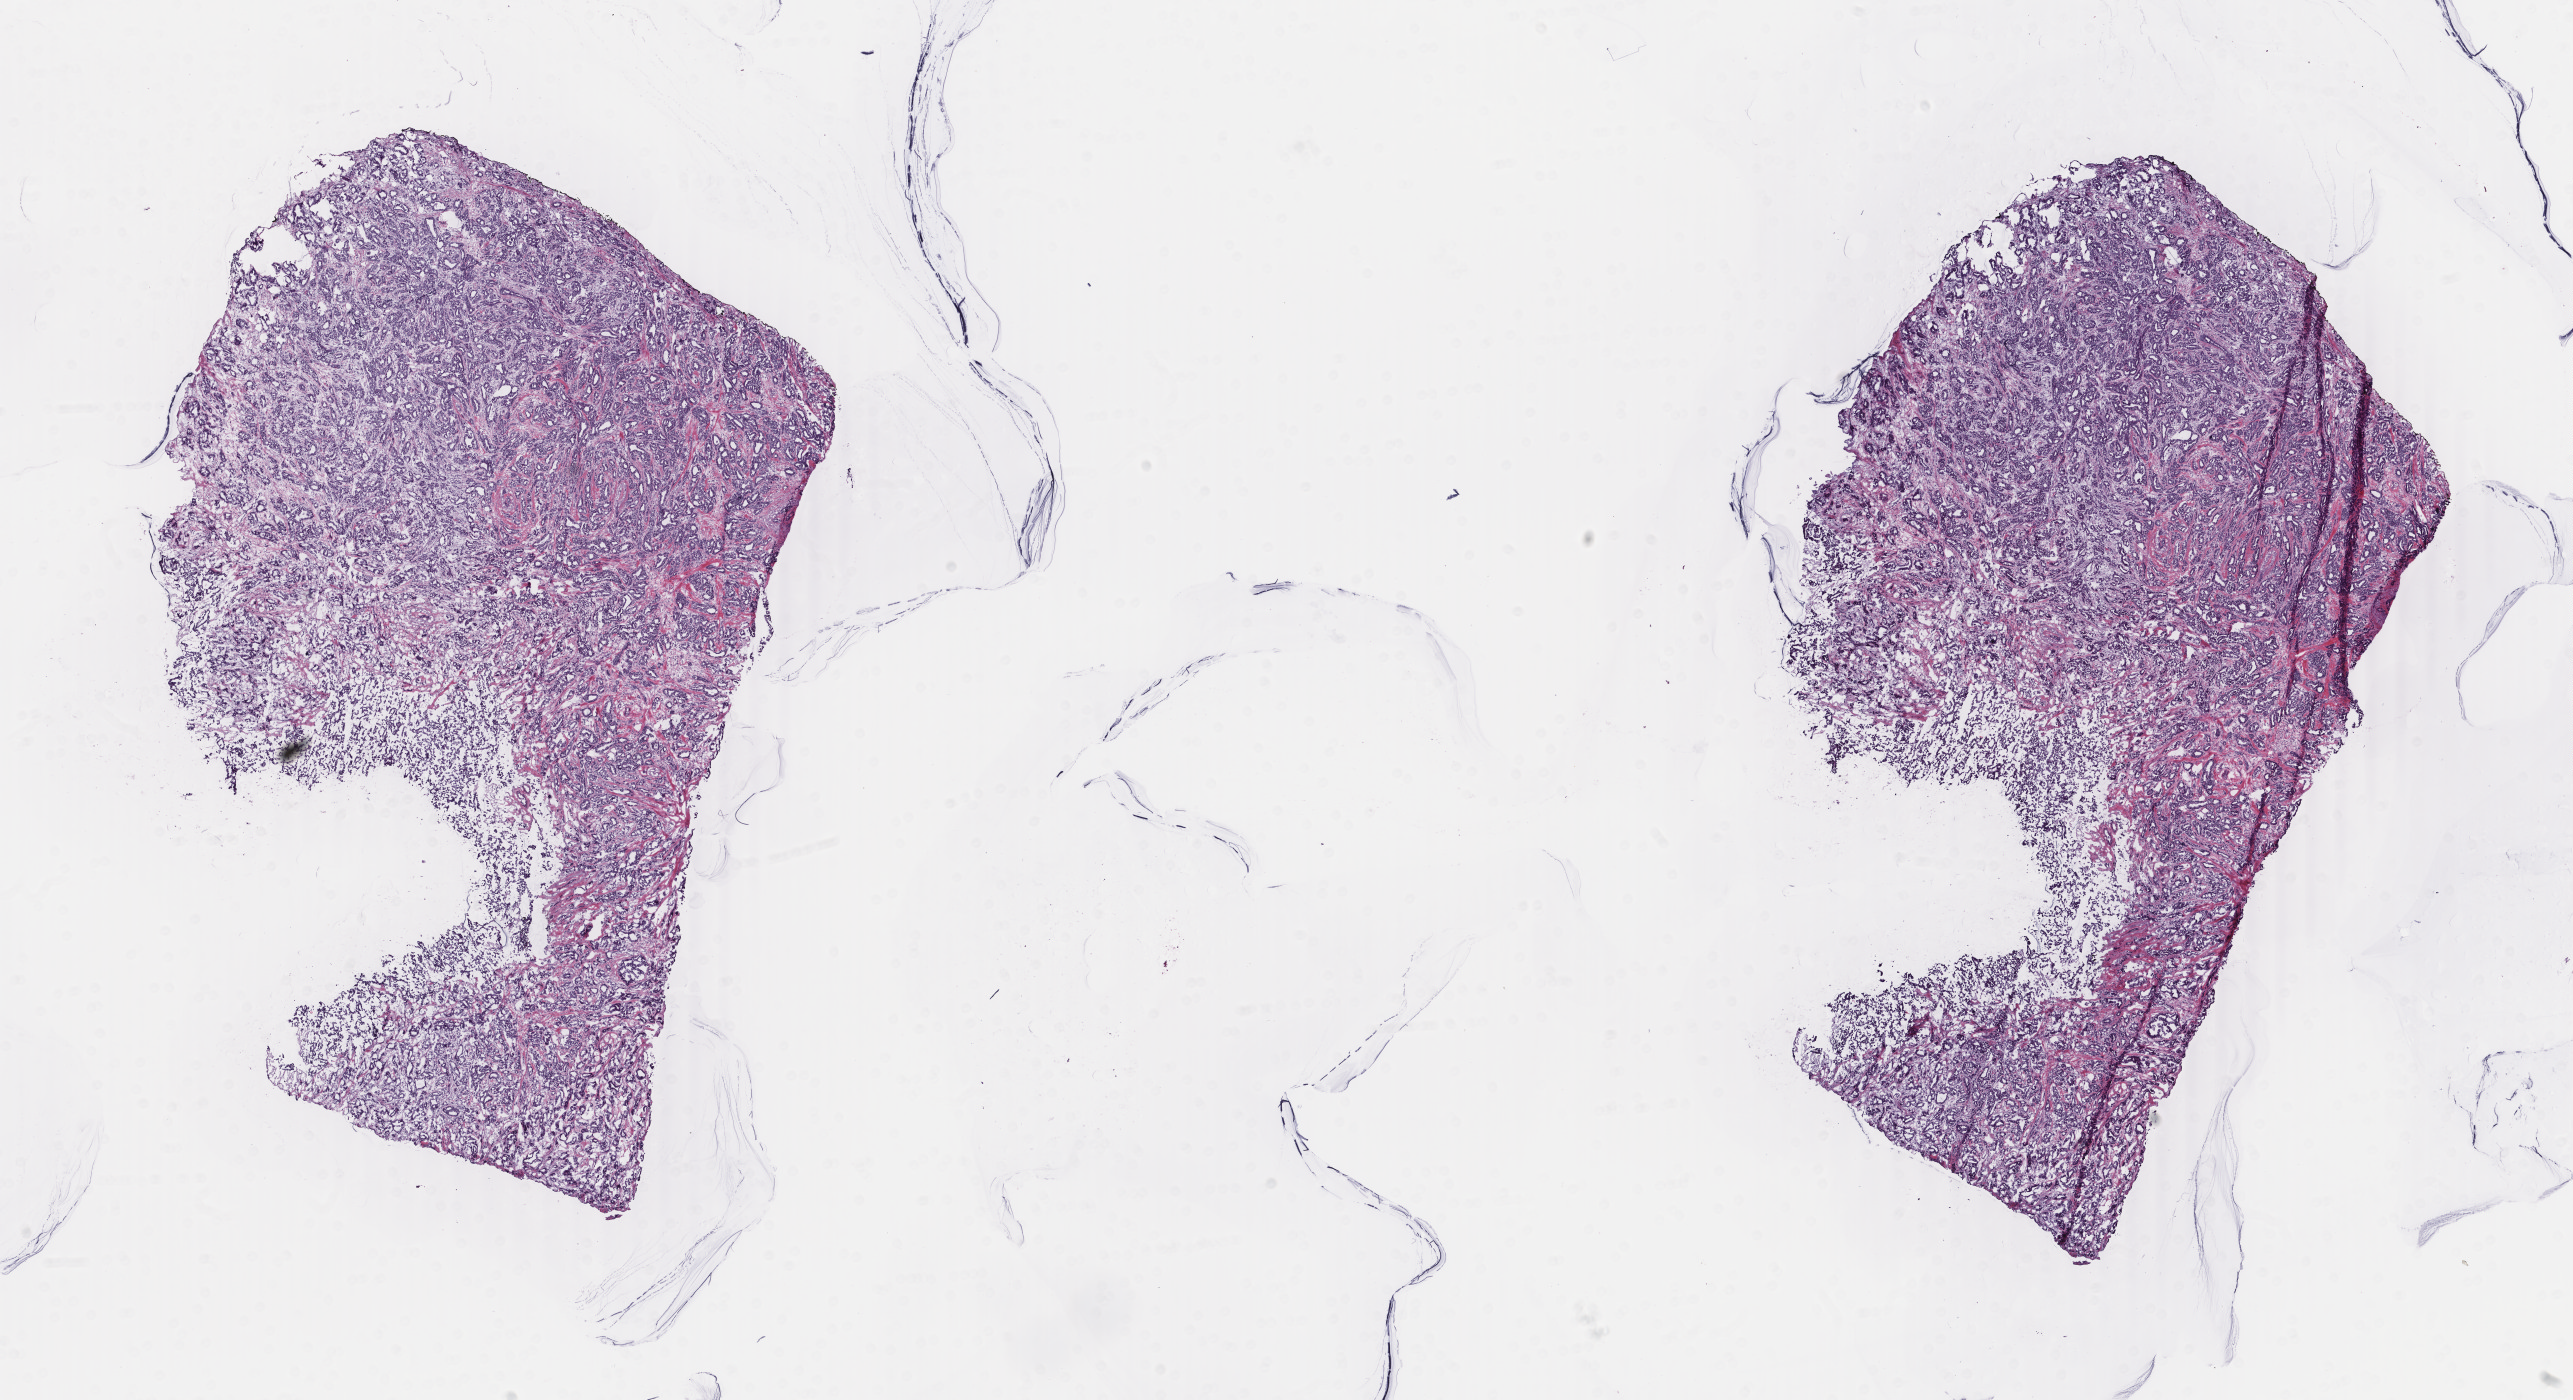
H&E-stained whole-slide image — shown as a low-resolution overview of the whole scanned area (about 20.5 x 11.1 mm), frozen section from the top of the tissue portion, breast, primary tumour sample. Female patient; age at initial diagnosis 79 years. Slide review estimates, as recorded: tumour cells 100%, tumour nuclei 70%.
Pathologic diagnosis: Infiltrating duct carcinoma, NOS.